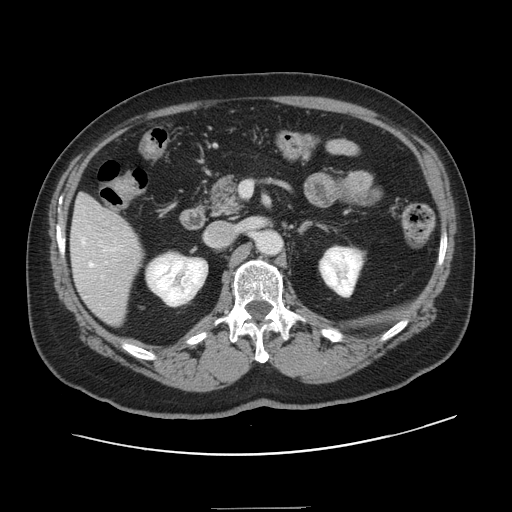
Contrast-enhanced abdominal CT, one axial slice. 120 kVp. Intravenous contrast given. Soft-tissue window (W 400 / L 40 HU). 2.5 mm slice thickness. 512 × 512 image matrix, field of view 402 × 402 mm. Male patient, age 62 years. Case-level facts recorded for this patient, not image findings: diagnosis: colorectal cancer liver metastases, imaged before liver resection; multiple liver metastases: yes; largest metastasis: 2.7 cm.
Structures marked on this image (expert manual segmentation):
- hepatic veins: bounding box (x1, y1, x2, y2) in pixels: (82, 238, 114, 267)
- liver: (72, 196, 142, 325)
- planned liver remnant (the part of the liver to remain after resection): (76, 196, 100, 214)
- portal vein (with intrahepatic branches): (100, 241, 115, 263)